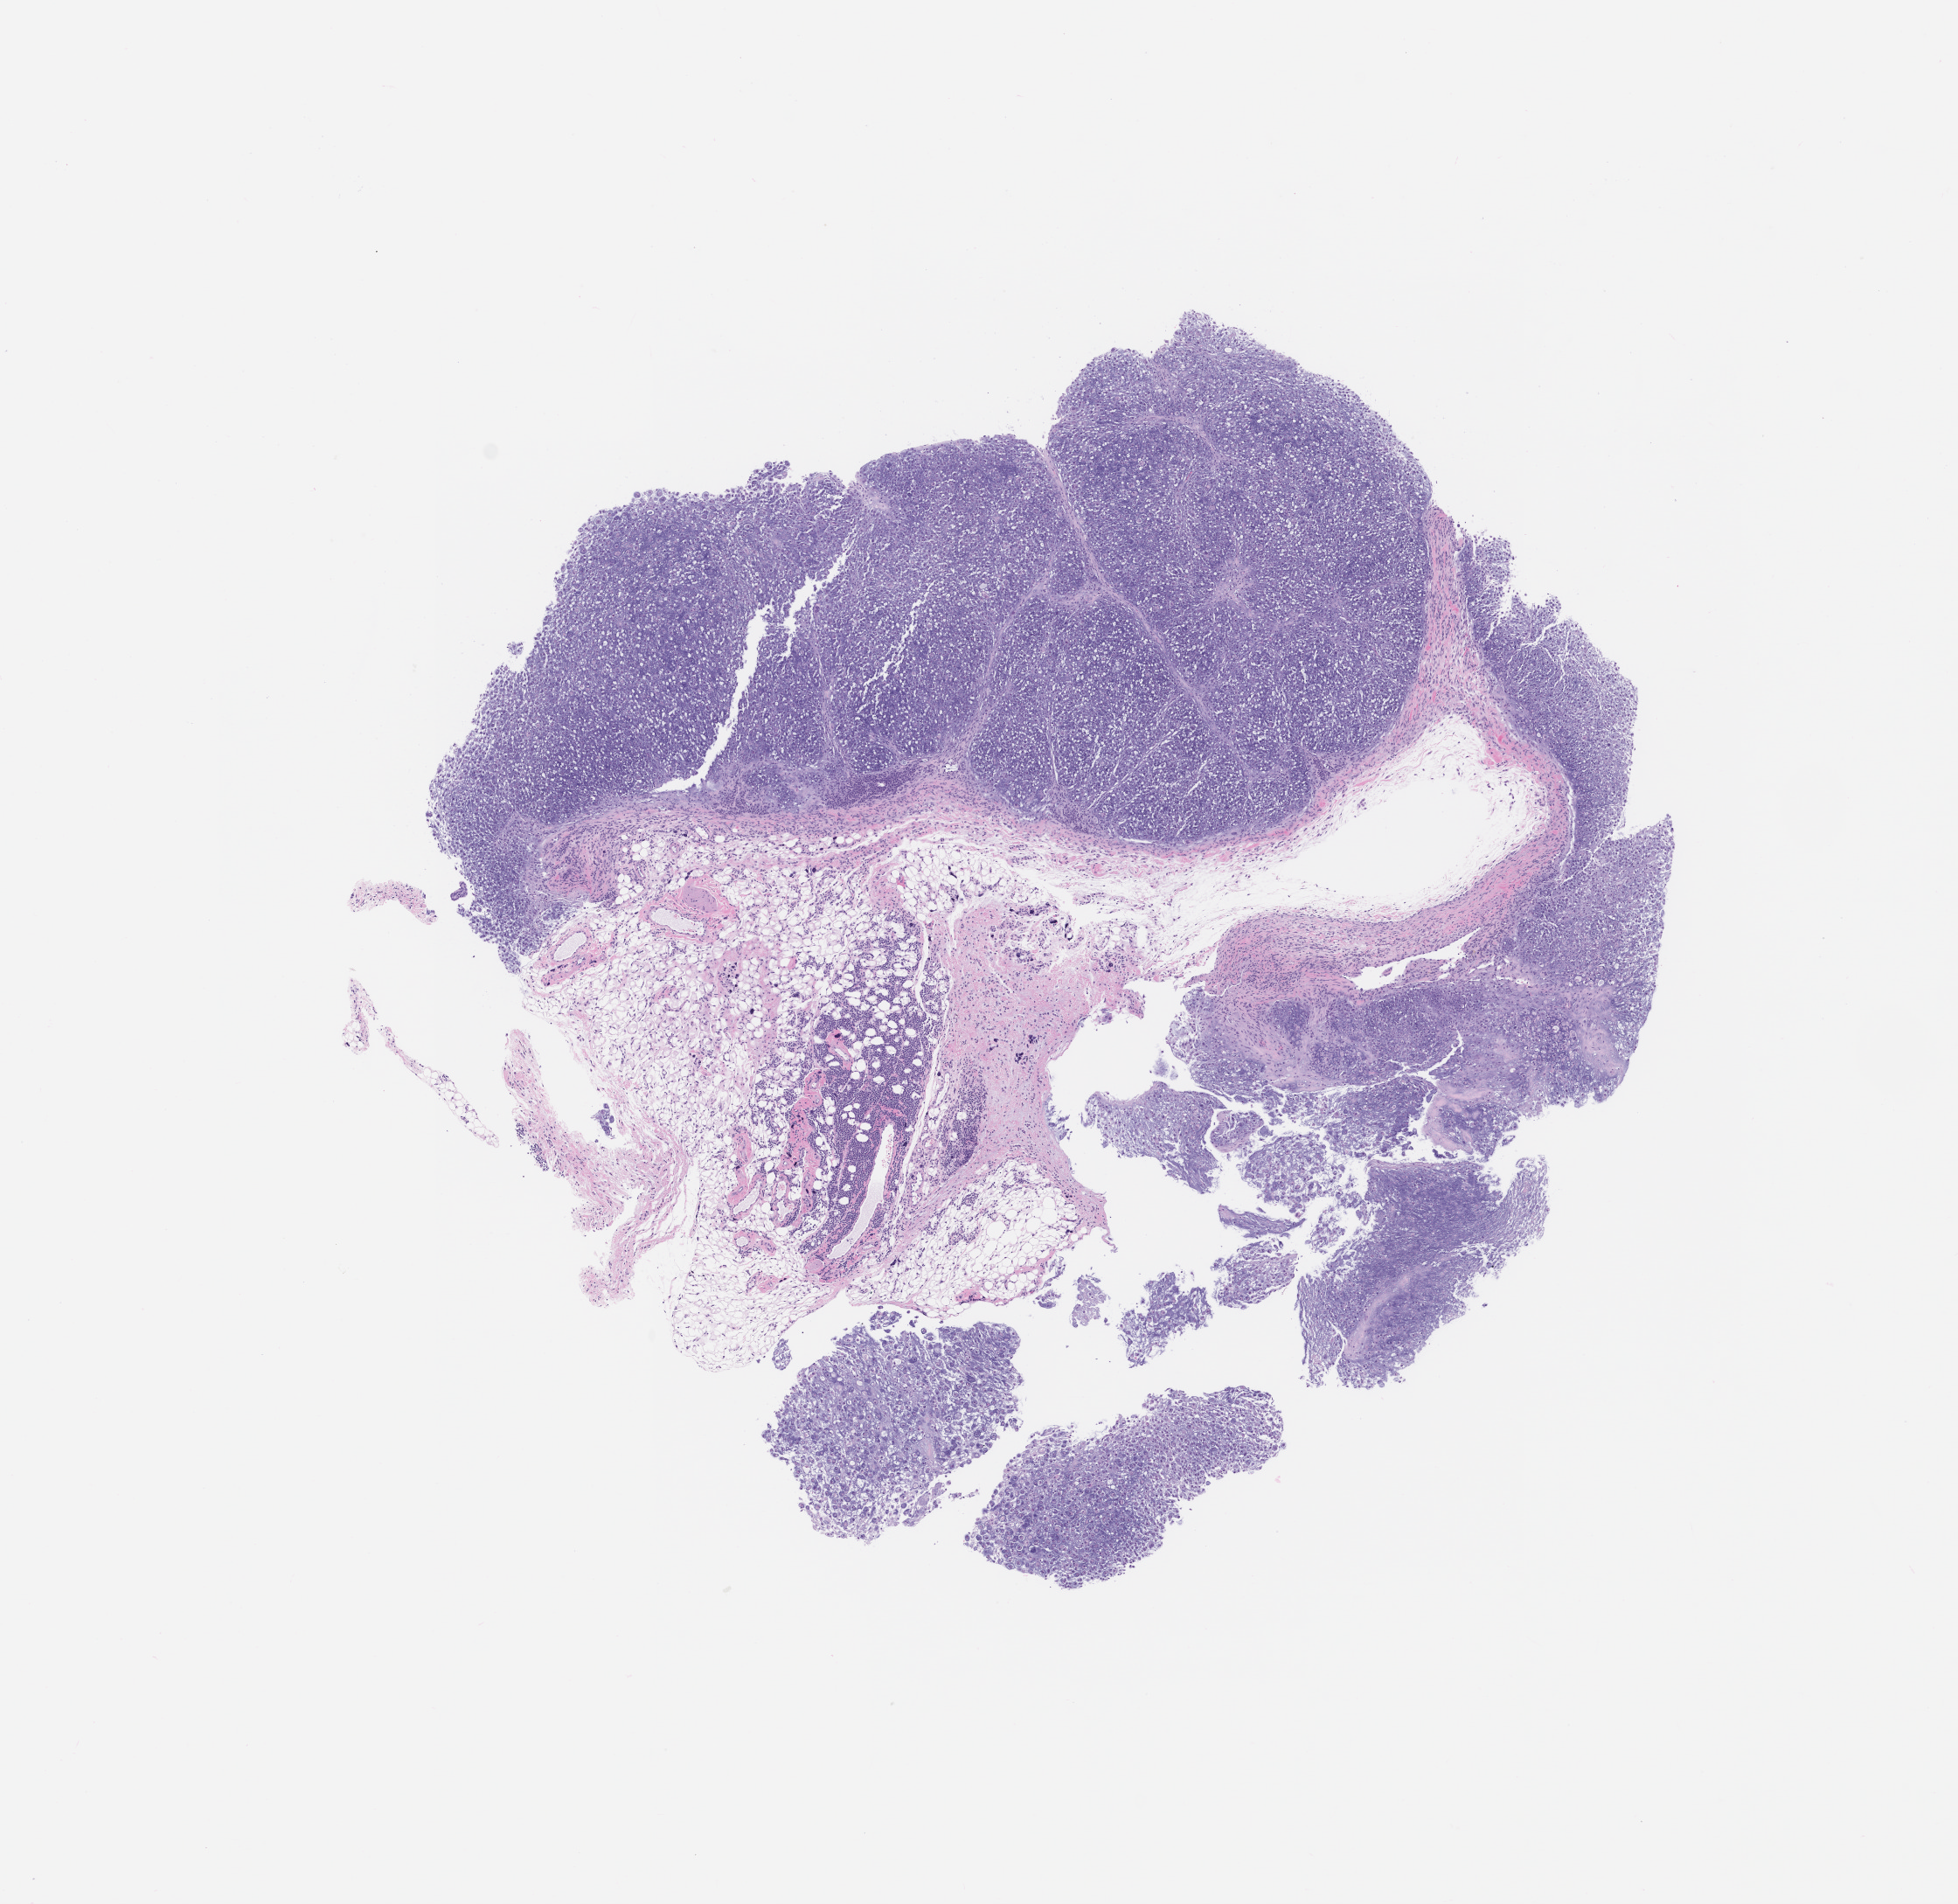
Whole-slide image, H&E: patient-derived xenograft (human tumor grown in a mouse), passage 0 — low-resolution overview of the scanned area, about 9.0 x 8.7 mm; FFPE section; originating tumor site category: musculoskeletal.
Originating patient diagnosis: Chondrosarcoma.